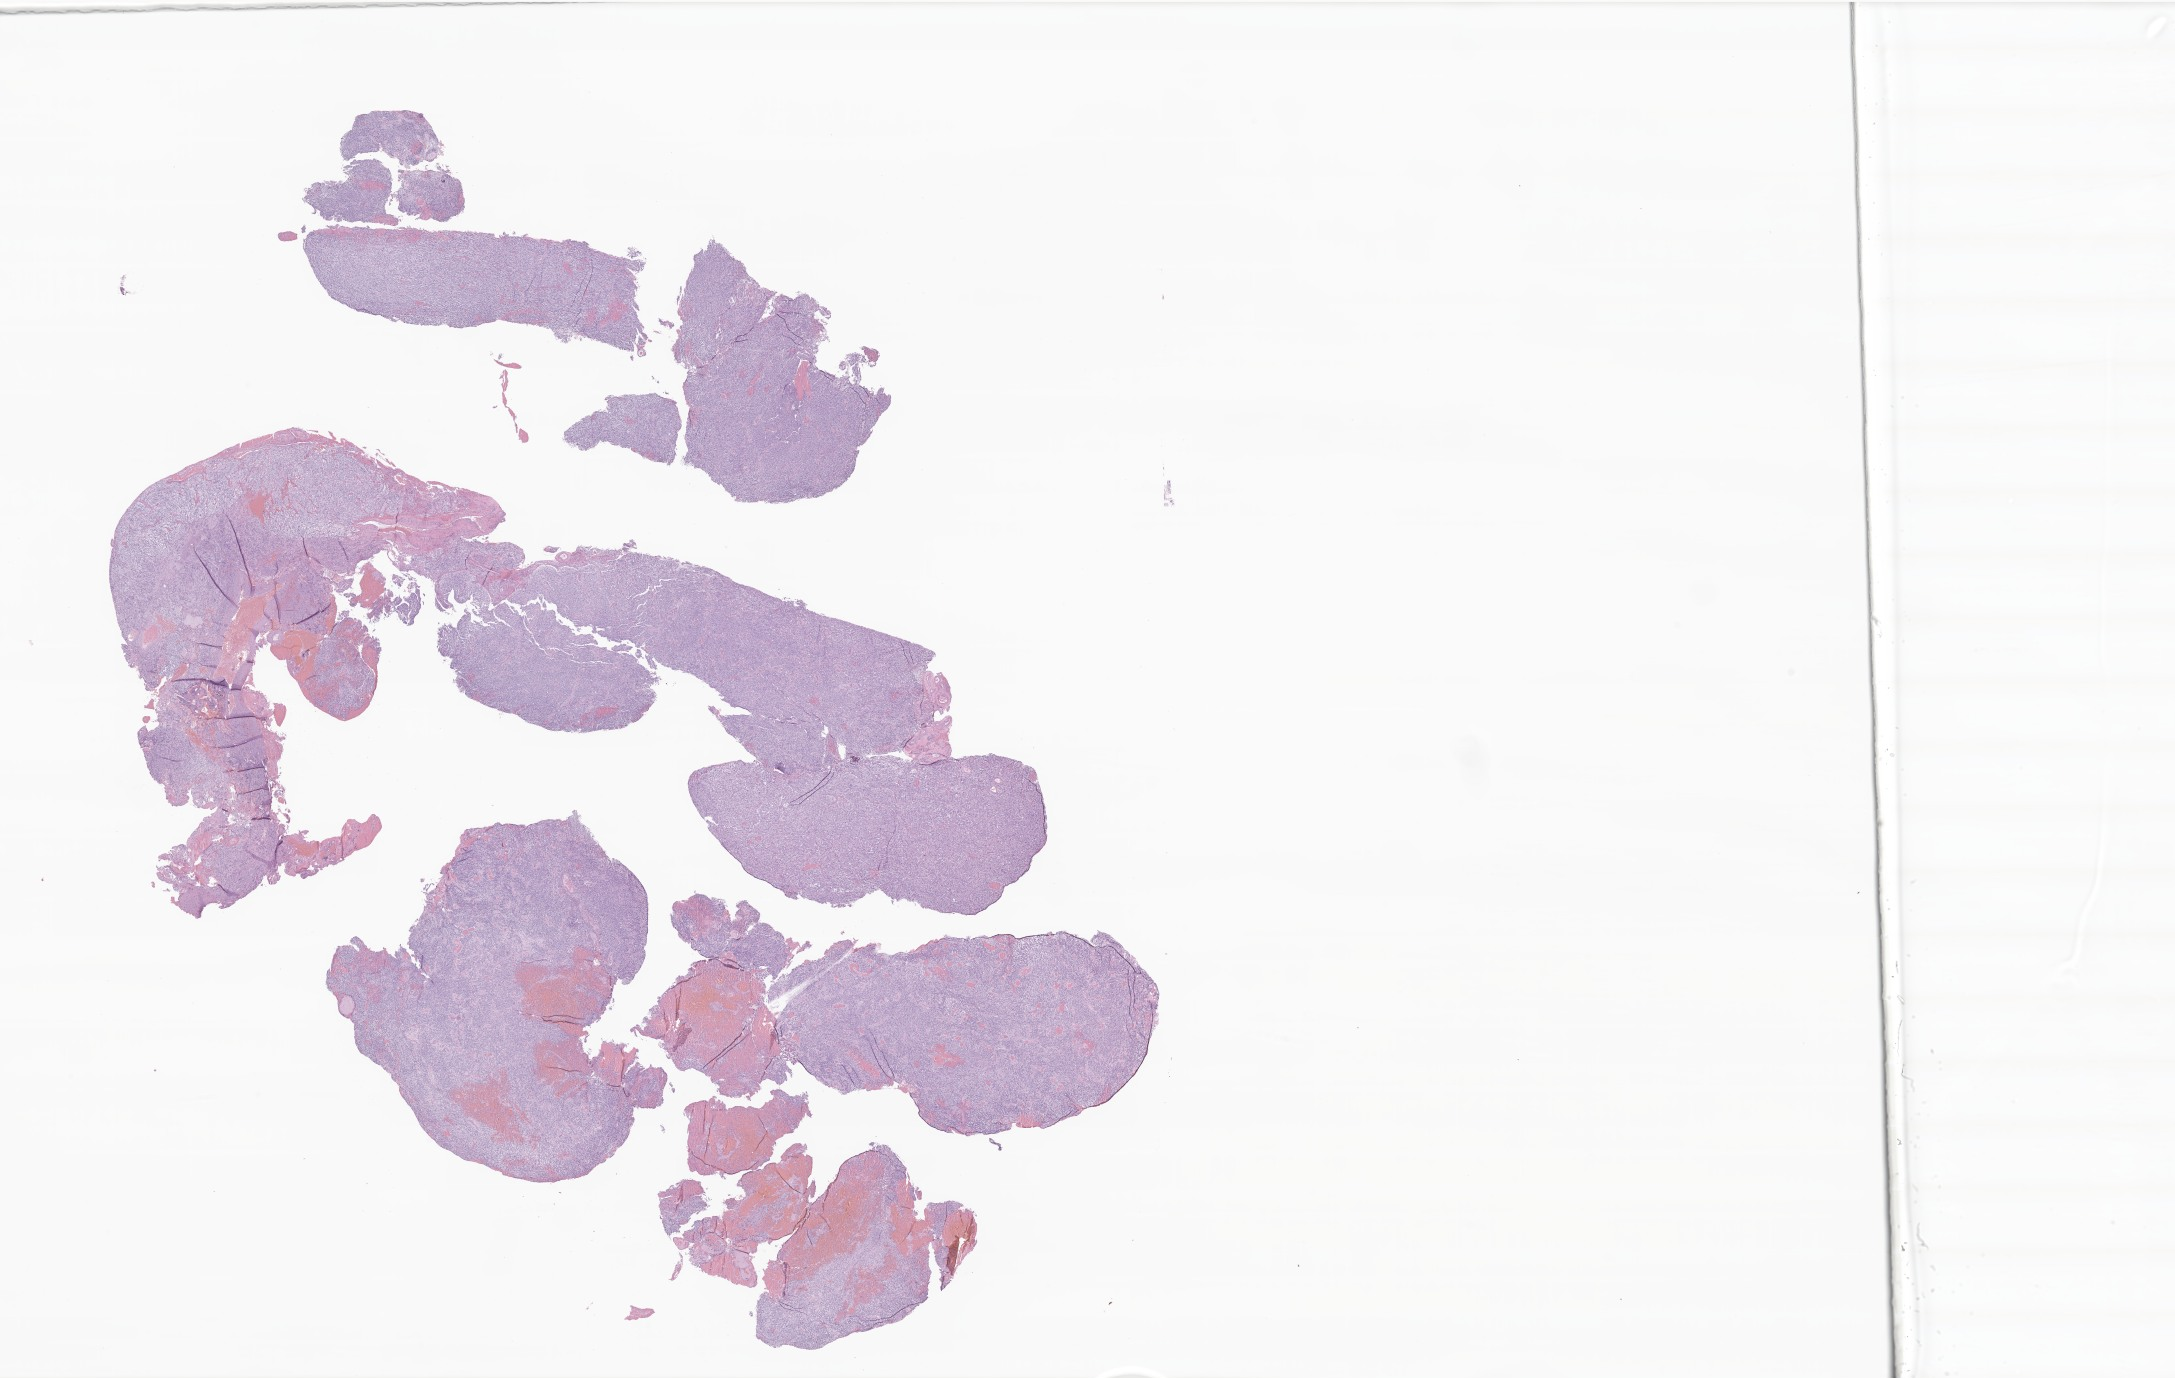
Hematoxylin and eosin (H&E) whole-slide image of tumor tissue from the brain, a low-resolution overview of the entire scanned area, about 36.7 x 23.2 mm; formalin-fixed paraffin-embedded section. Patient: male, age 168 months (14 years).
Diagnosis: Astrocytoma, NOS.